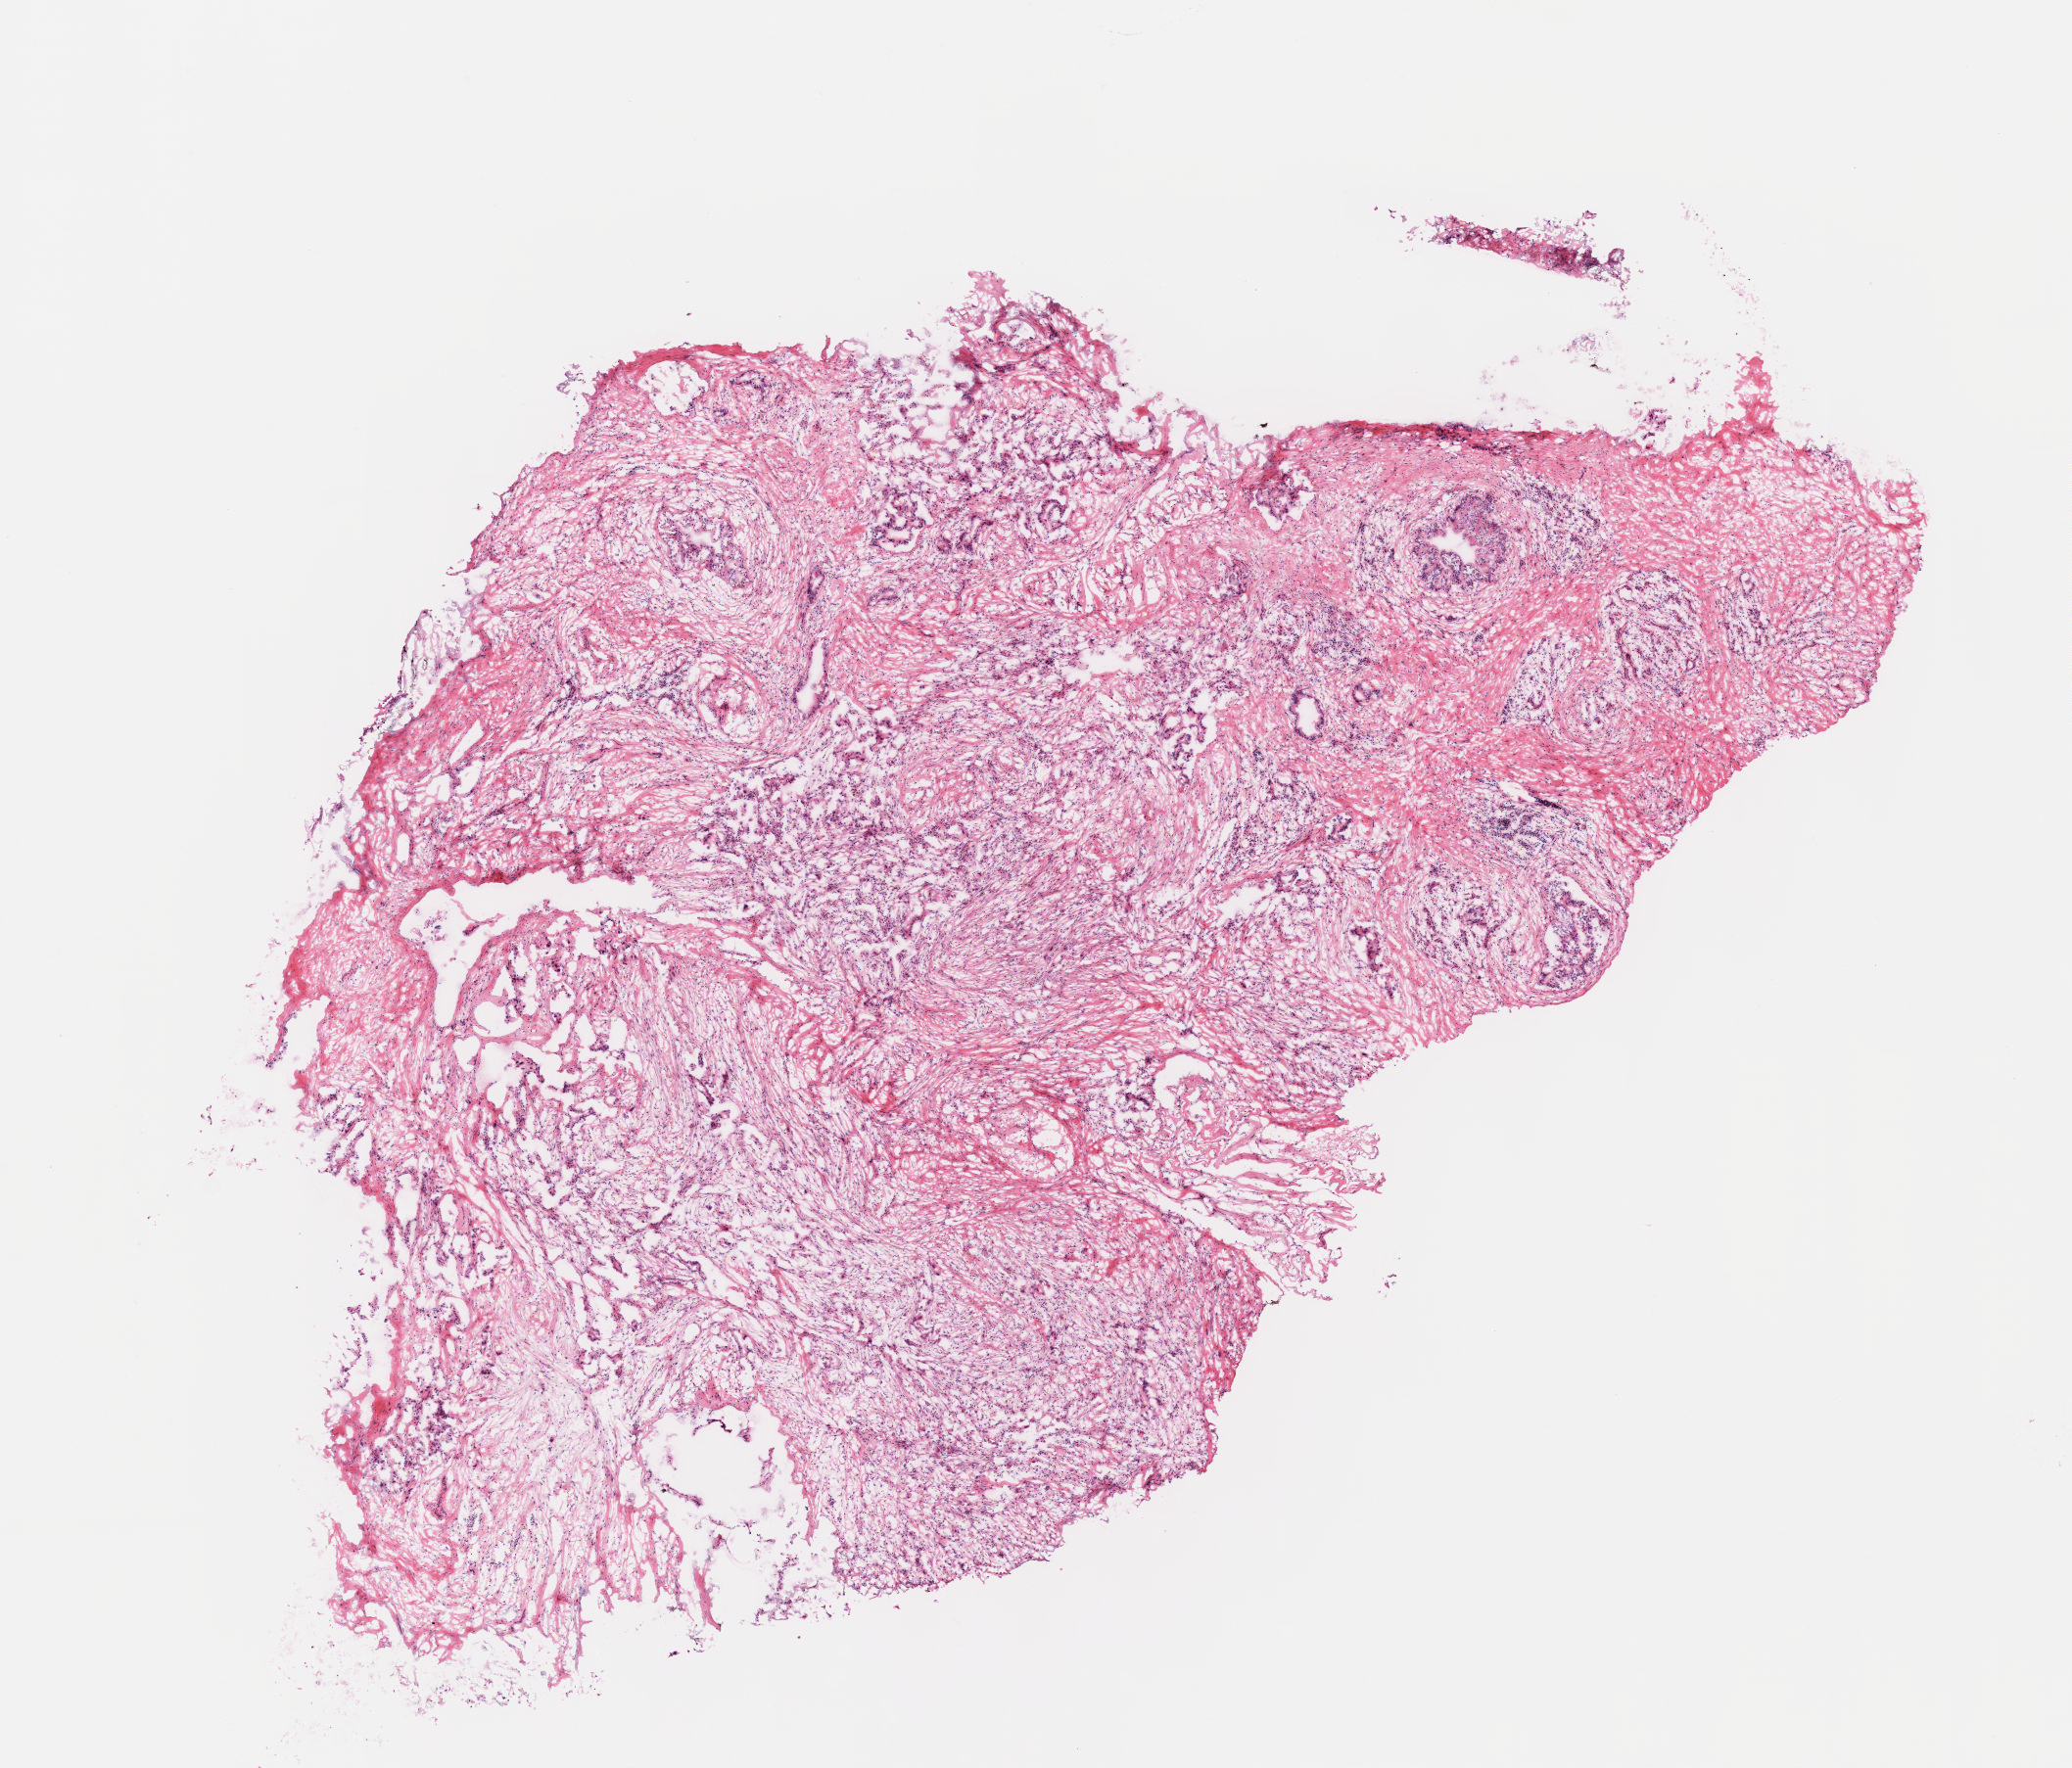
Digitized Hematoxylin and eosin (H&E) stained tissue section (whole slide), low-resolution overview of the scanned area, about 8.6 x 7.3 mm. FFPE section. Primary tumour sample from the pancreas. Patient: female, age at initial diagnosis 62 years. Histologic grade: G2 (moderately differentiated).
Lymph nodes positive (case pathology): 1 of 7 examined. AJCC pathologic stage: IIB. Pathologic diagnosis: Infiltrating duct carcinoma, NOS (head of pancreas).